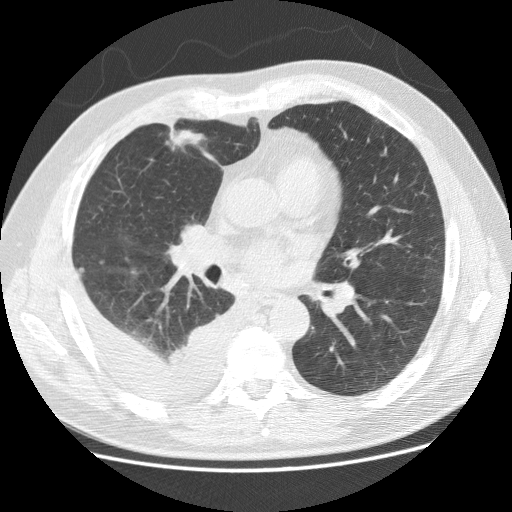
Axial slice from a low-dose chest CT screening exam. First (baseline) screen. Lung window (W 1500 / L -600 HU). Male participant, aged 65 years at enrolment. Current smoker at enrolment.
- Lesion marked by an expert reader, bounding box [x1, y1, x2, y2] px = [148, 120, 217, 170].
- The exam's reader record, not a measurement of the box and not confirmed to be the same lesion: non-calcified nodule or mass ≥4 mm, right middle lobe, 22 × 15 mm, spiculated (stellate) margins, mixed attenuation.
- Official screen result: positive, change unspecified: nodule(s) >= 4 mm or enlarging nodule(s), mass(es), or other non-specific abnormalities suspicious for lung cancer.
- Lung cancer was diagnosed 4 days after this screen: adenocarcinoma, NOS, right middle lobe, stage IV (AJCC 6th edition), 20 mm at pathology.